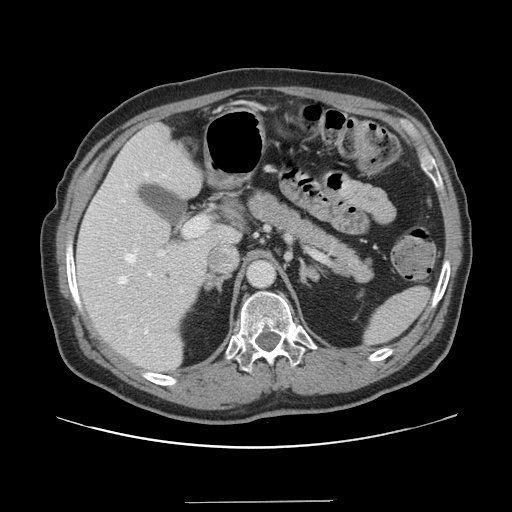
Contrast-enhanced abdominal CT, one axial slice. Slice 93 of 151 in the series (ordered by position). Soft-tissue window (W 400 / L 40 HU). 2.5 mm slice thickness. 512 × 512 image matrix, field of view 399 × 399 mm. Male patient, age 63 years. From the clinical record (not read from this slice): diagnosis: colorectal cancer liver metastases, imaged before liver resection; multiple liver metastases: no; largest metastasis: 2.1 cm.
Outlined on this slice (outlined manually by an expert reader):
- hepatic veins: bounding box <118,172,182,351> (left, top, right, bottom; pixels)
- liver: <77,125,239,373>
- planned liver remnant (the part of the liver to remain after resection): <76,125,239,373>
- portal vein (with intrahepatic branches): <157,217,207,256>